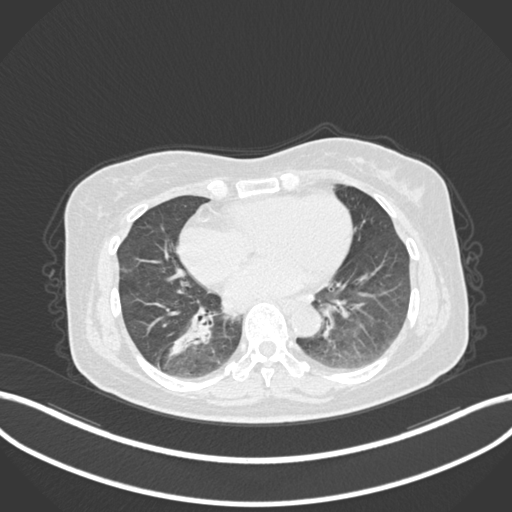
Chest CT, one axial slice; position 59 of 222 along the scan axis; reconstruction kernel B30f; 120 kVp; lung window (W 1500 / L -600 HU); 1 mm slice thickness; 512 × 512 image matrix, field of view 400 × 400 mm. Patient: female, 67 years. Case-level facts recorded for this patient, not image findings: clinical TNM (as recorded): T1c N1 M0; histopathological grade: G2-3.
Outlined on this slice (rectangle marked by the reading radiologist):
- lung tumour (recorded histology: adenocarcinoma): box from (x=162, y=300) to (x=215, y=364) px